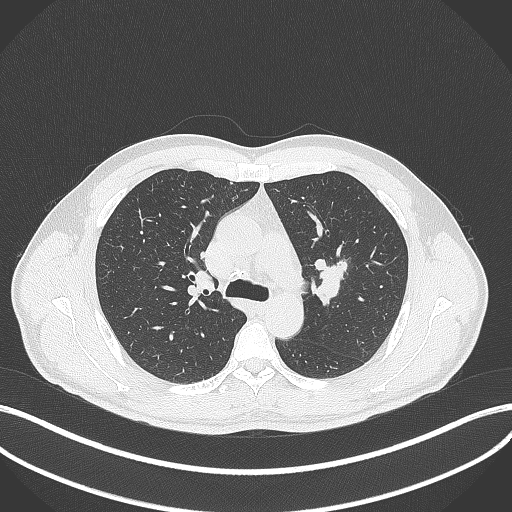
Chest CT, one axial slice; position 281 of 392 along the scan axis; reconstruction kernel B70f; 120 kVp; lung window (W 1500 / L -600 HU); 1 mm slice thickness; 512 × 512 image matrix, field of view 400 × 400 mm. Male patient, age 50 years. From the clinical record (not read from this slice): clinical TNM (as recorded): T1c N1 M1b.
Annotated regions visible in this slice (bounding box drawn by a radiologist):
- lung tumour (recorded histology: squamous cell carcinoma): box from (x=307, y=258) to (x=351, y=306) px